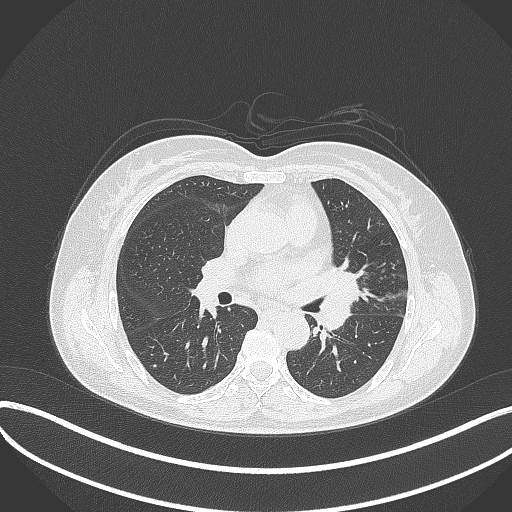
Chest CT, one axial slice; slice 191 of 373 in the series (ordered by position); reconstruction kernel B70f; 120 kVp; lung window (W 1500 / L -600 HU); 512 × 512 image matrix, field of view 400 × 400 mm. Patient: female, 54 years. Case-level facts recorded for this patient, not image findings: clinical TNM (as recorded): T2a N1 M0; histopathological grade: G3.
Annotated regions visible in this slice (rectangle marked by the reading radiologist):
- lung tumour (recorded histology: small cell carcinoma): bounding box [x1, y1, x2, y2] px = [315, 256, 362, 339]